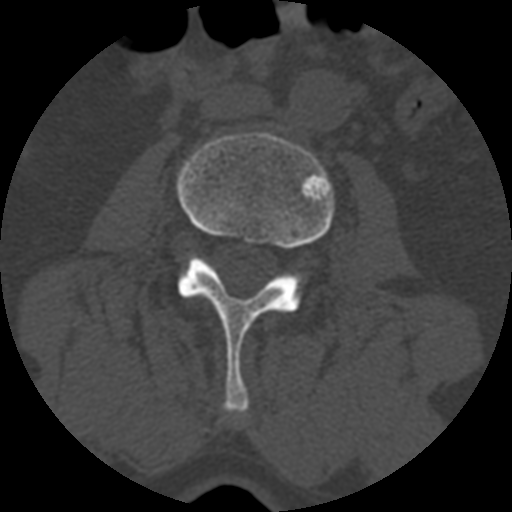
CT including the spine, one axial slice. Slice 305 of 399 in the series (ordered by position). Reconstruction kernel STANDARD. 120 kVp. Bone window (W 1800 / L 400 HU). 512 × 512 image matrix, field of view 160 × 160 mm. Patient age 71 years. From the clinical record (not read from this slice): primary cancer: prostate.
Outlined on this slice (semi-automatic segmentation, software-assisted and operator-edited):
- L3 vertebra: box from (x=175, y=130) to (x=335, y=415) px